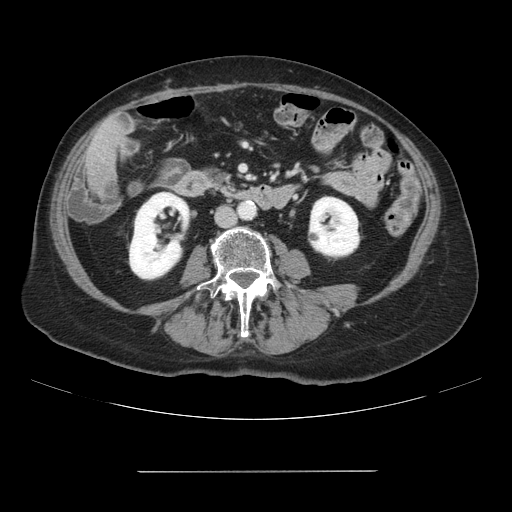
Contrast-enhanced abdominal CT, one axial slice; slice 9 of 111 in the series (ordered by position); intravenous contrast given; soft-tissue window (W 400 / L 40 HU); 512 × 512 image matrix. Female patient, age 74 years. Case-level facts recorded for this patient, not image findings: diagnosis: colorectal cancer liver metastases, imaged before liver resection; multiple liver metastases: yes; largest metastasis: 1.1 cm; disease in both lobes: yes.
Structures marked on this image (manually delineated by an expert):
- liver: bounding box (x1, y1, x2, y2) in pixels: (87, 119, 123, 190)